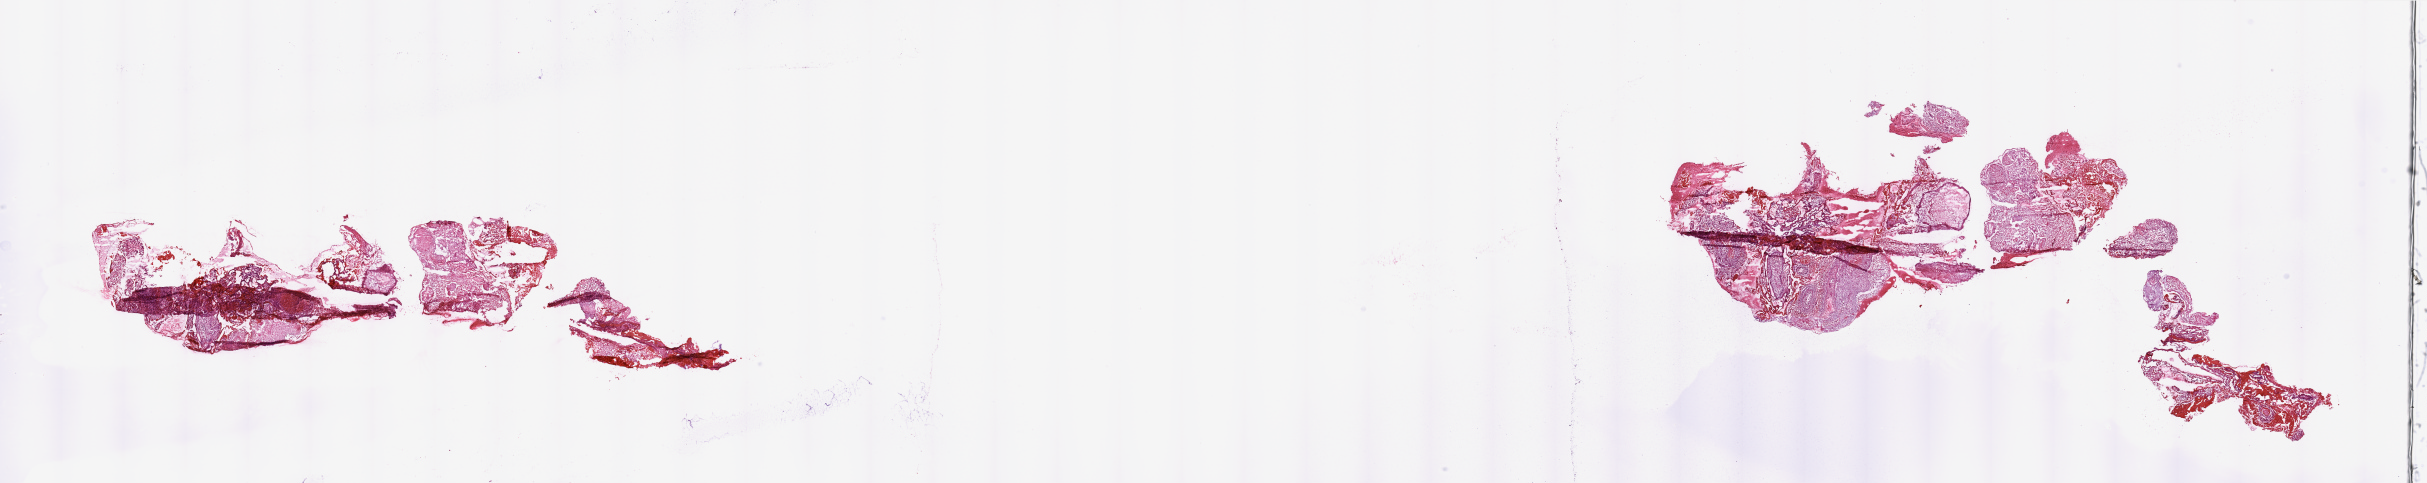
H&E whole-slide image, low-resolution overview of the scanned area, about 38.4 x 7.6 mm. Tumour tissue sample, brain. Male, 61 y/o.
Patient diagnosis (cohort enrolment): glioblastoma multiforme (brain). Primary tumour site (as recorded): frontal lobe.